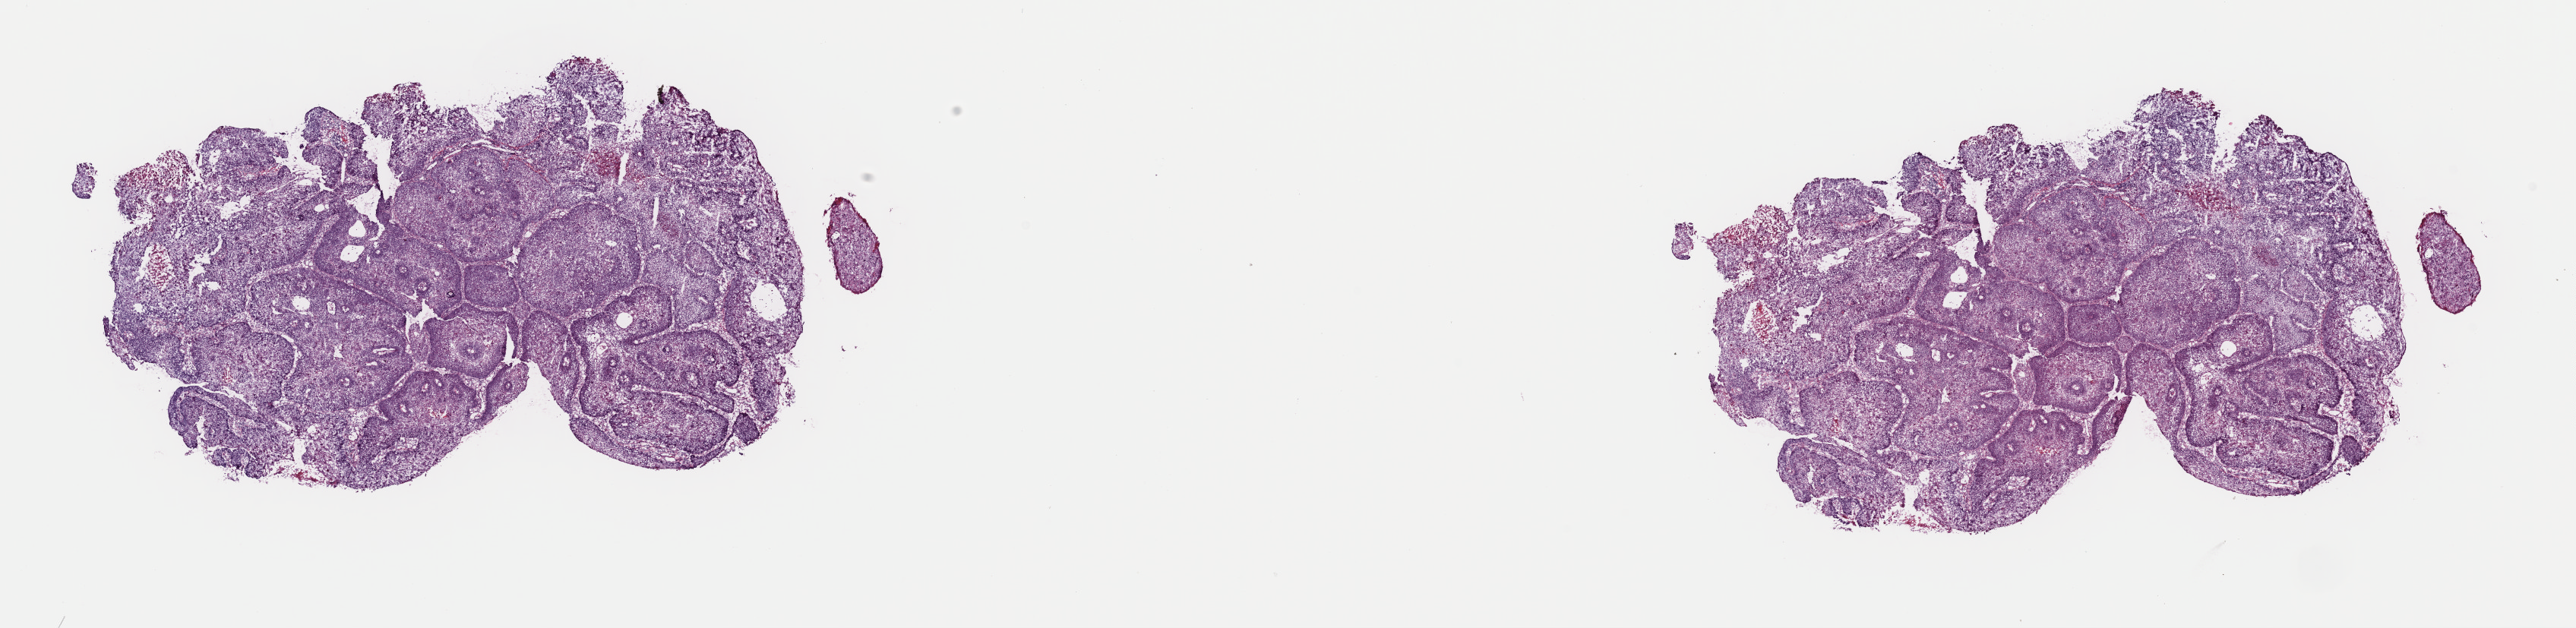
Whole-slide histology image, Hematoxylin and eosin (H&E) stained, shown as a low-resolution overview of the whole scanned area (about 26.8 x 6.5 mm); frozen section from the top of the tissue portion; sample: primary tumour, esophagus. Female patient; age at initial diagnosis 69 years. Pathologist review of this section (percent, as recorded): tumour cells 87%, tumour nuclei 85%.
Diagnosis: Squamous cell carcinoma, NOS (lower third of esophagus).